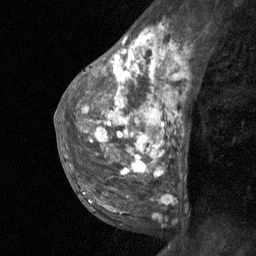
Breast MRI (dynamic contrast-enhanced), one sagittal slice; position 37 of 64 along the scan axis; dynamic contrast-enhanced study with each time point stored as its own series, time point 2 of 3 at this slice position (early post-contrast, ordered by acquisition time); 1.5 T; TE 4.8 ms, TR 27 ms; 2 mm slice thickness; 256 × 256 image matrix, field of view 180 × 180 mm. Patient: female, 36 years. Case-level facts recorded for this patient, not image findings: setting: breast cancer imaged before/during neoadjuvant chemotherapy; receptor status: HR-positive, HER2-negative.
Structures marked on this image (semi-automatically segmented with operator editing):
- analysis volume of interest (the breast-tissue region the enhancement analysis was run in; not a lesion): bounding box <67,12,180,226> (left, top, right, bottom; pixels)
- tumour enhancement mask (voxels above the 90 % enhancement threshold inside the analysis volume of interest): <83,30,156,171>